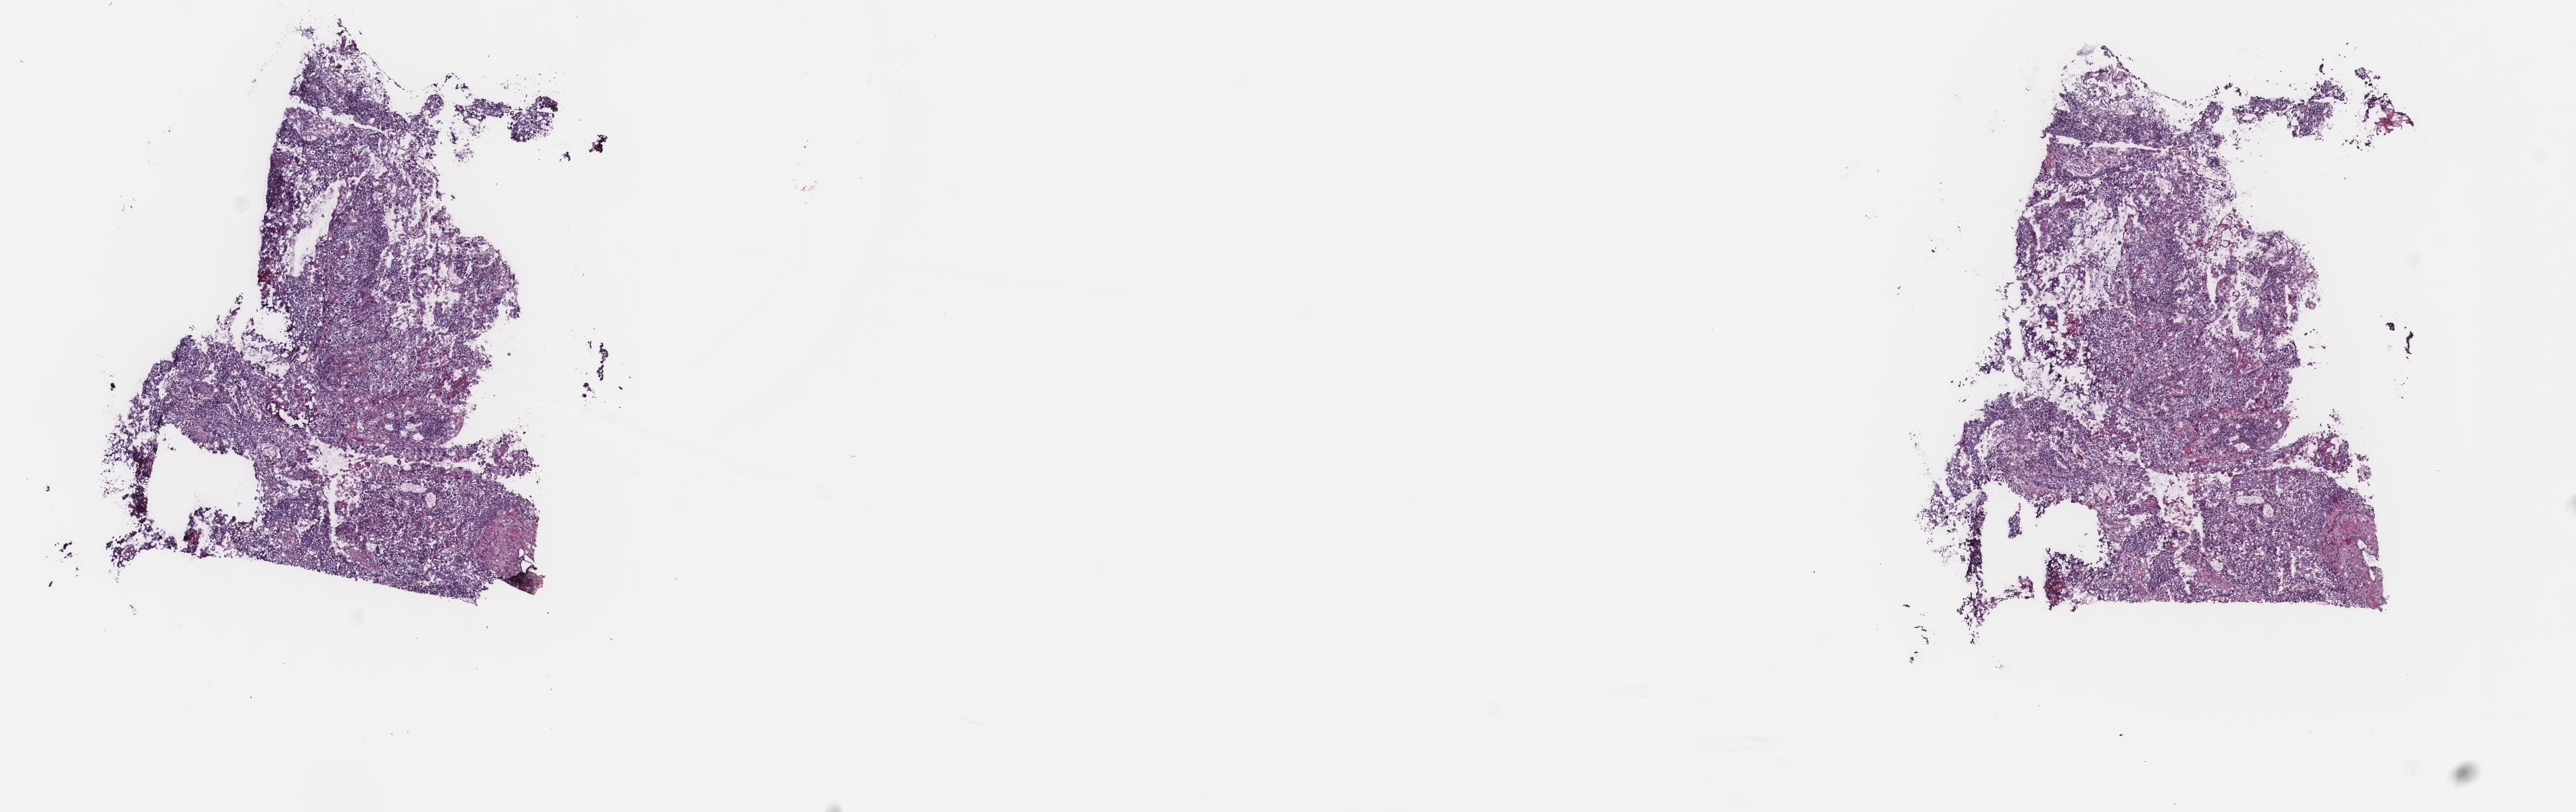
Digitized H&E tissue section (whole slide) — shown as a low-resolution overview of the whole scanned area (about 15.1 x 4.8 mm), frozen section, sample: primary tumour, lung. Female patient; age at initial diagnosis 73 years. Composition of this section per pathologist review: tumour cells 98%, tumour nuclei 85%, normal cells 0%, stromal cells 2%, necrosis 0%. Infiltration values recorded for this section: lymphocyte infiltration 0%, monocyte infiltration 0%, neutrophil infiltration 0%.
* AJCC pathologic stage: IIIA (7th edition)
* TNM: T3 N1 M0
* diagnosis: Squamous cell carcinoma, NOS (lower lobe, lung)